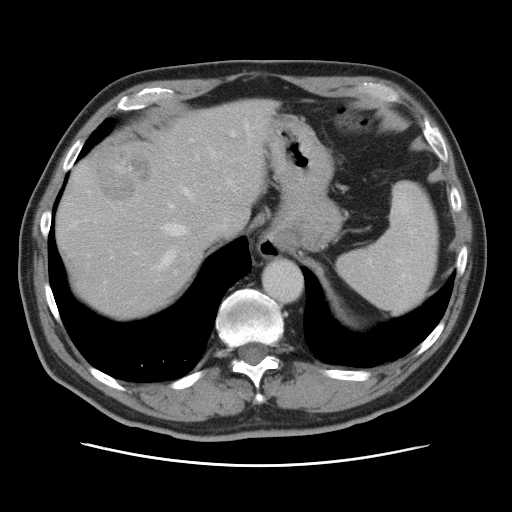
Contrast-enhanced abdominal CT, one axial slice; position 62 of 80 along the scan axis; intravenous contrast given; soft-tissue window (W 400 / L 40 HU); 512 × 512 image matrix, field of view 370 × 370 mm. Male patient, age 69 years. Case-level facts recorded for this patient, not image findings: diagnosis: colorectal cancer liver metastases, imaged before liver resection; multiple liver metastases: no; largest metastasis: 5 cm; disease in both lobes: yes.
Outlined on this slice (outlined manually by an expert reader):
- hepatic veins: box from (x=156, y=124) to (x=252, y=270) px
- liver: (x=57, y=98)–(x=274, y=321)
- planned liver remnant (the part of the liver to remain after resection): (x=57, y=98)–(x=274, y=322)
- portal vein (with intrahepatic branches): (x=134, y=130)–(x=235, y=273)
- liver metastasis: (x=93, y=153)–(x=151, y=203)